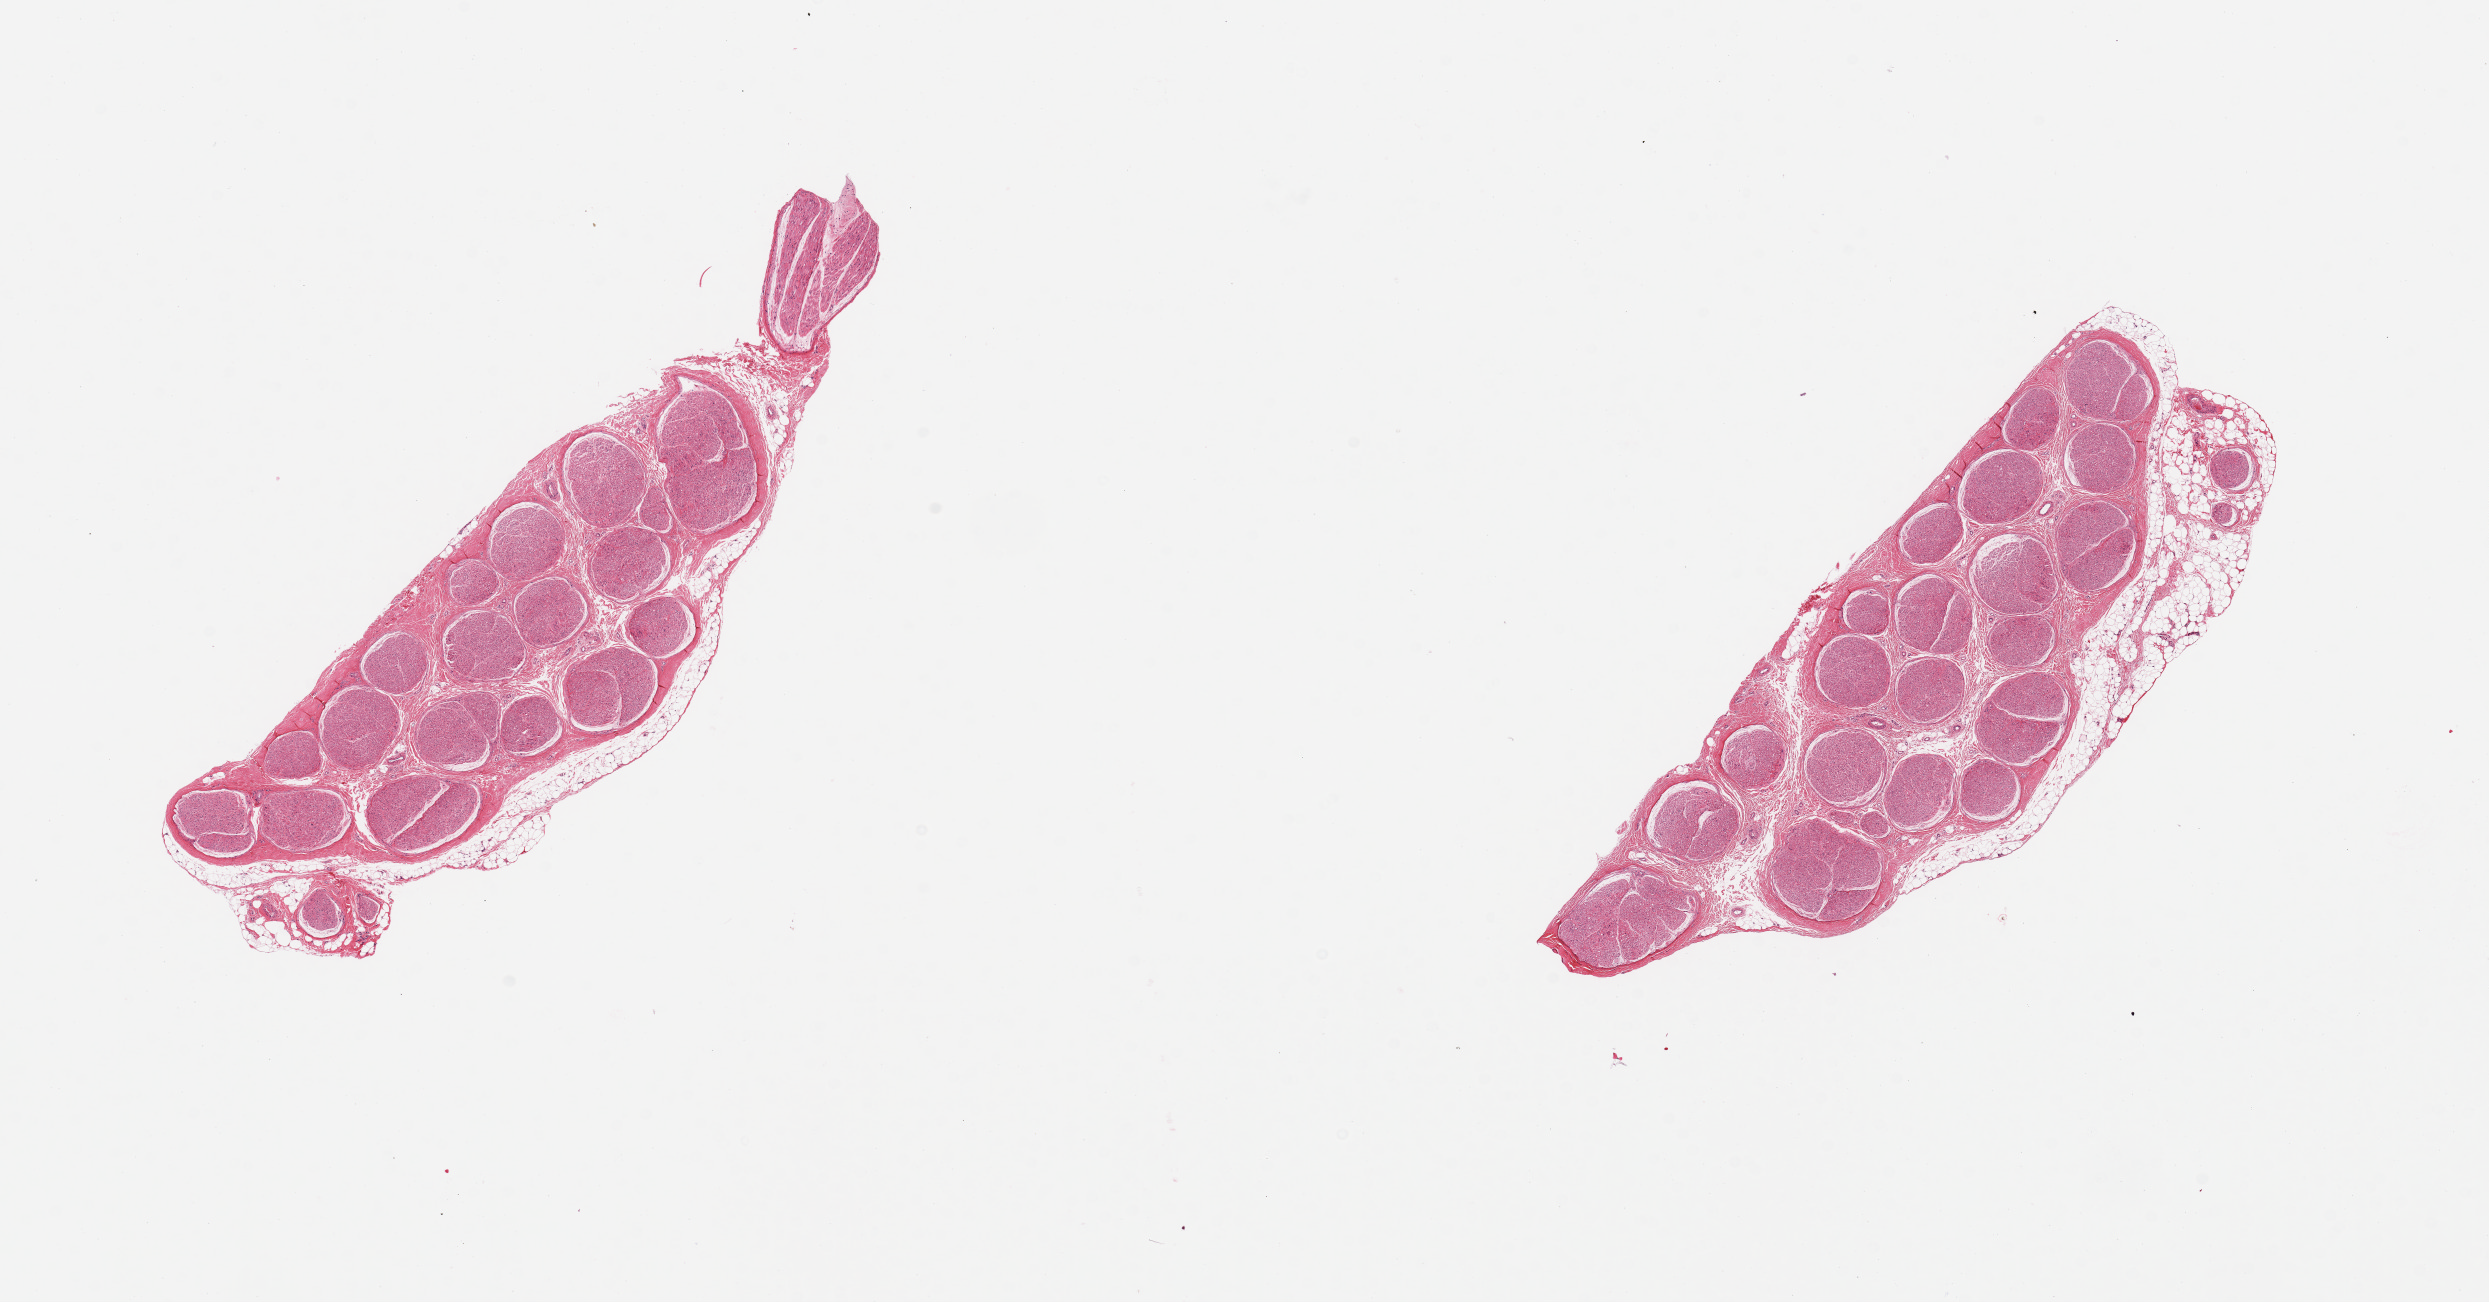
Haematoxylin and eosin whole-slide image, low-resolution overview of the scanned area, about 19.7 x 10.3 mm, PAXgene-fixed, paraffin-embedded tissue, sampled site (target tissue): tibial nerve, donor tissue sample. Female donor.
• review note (as recorded): 2 pieces; 20% external fat